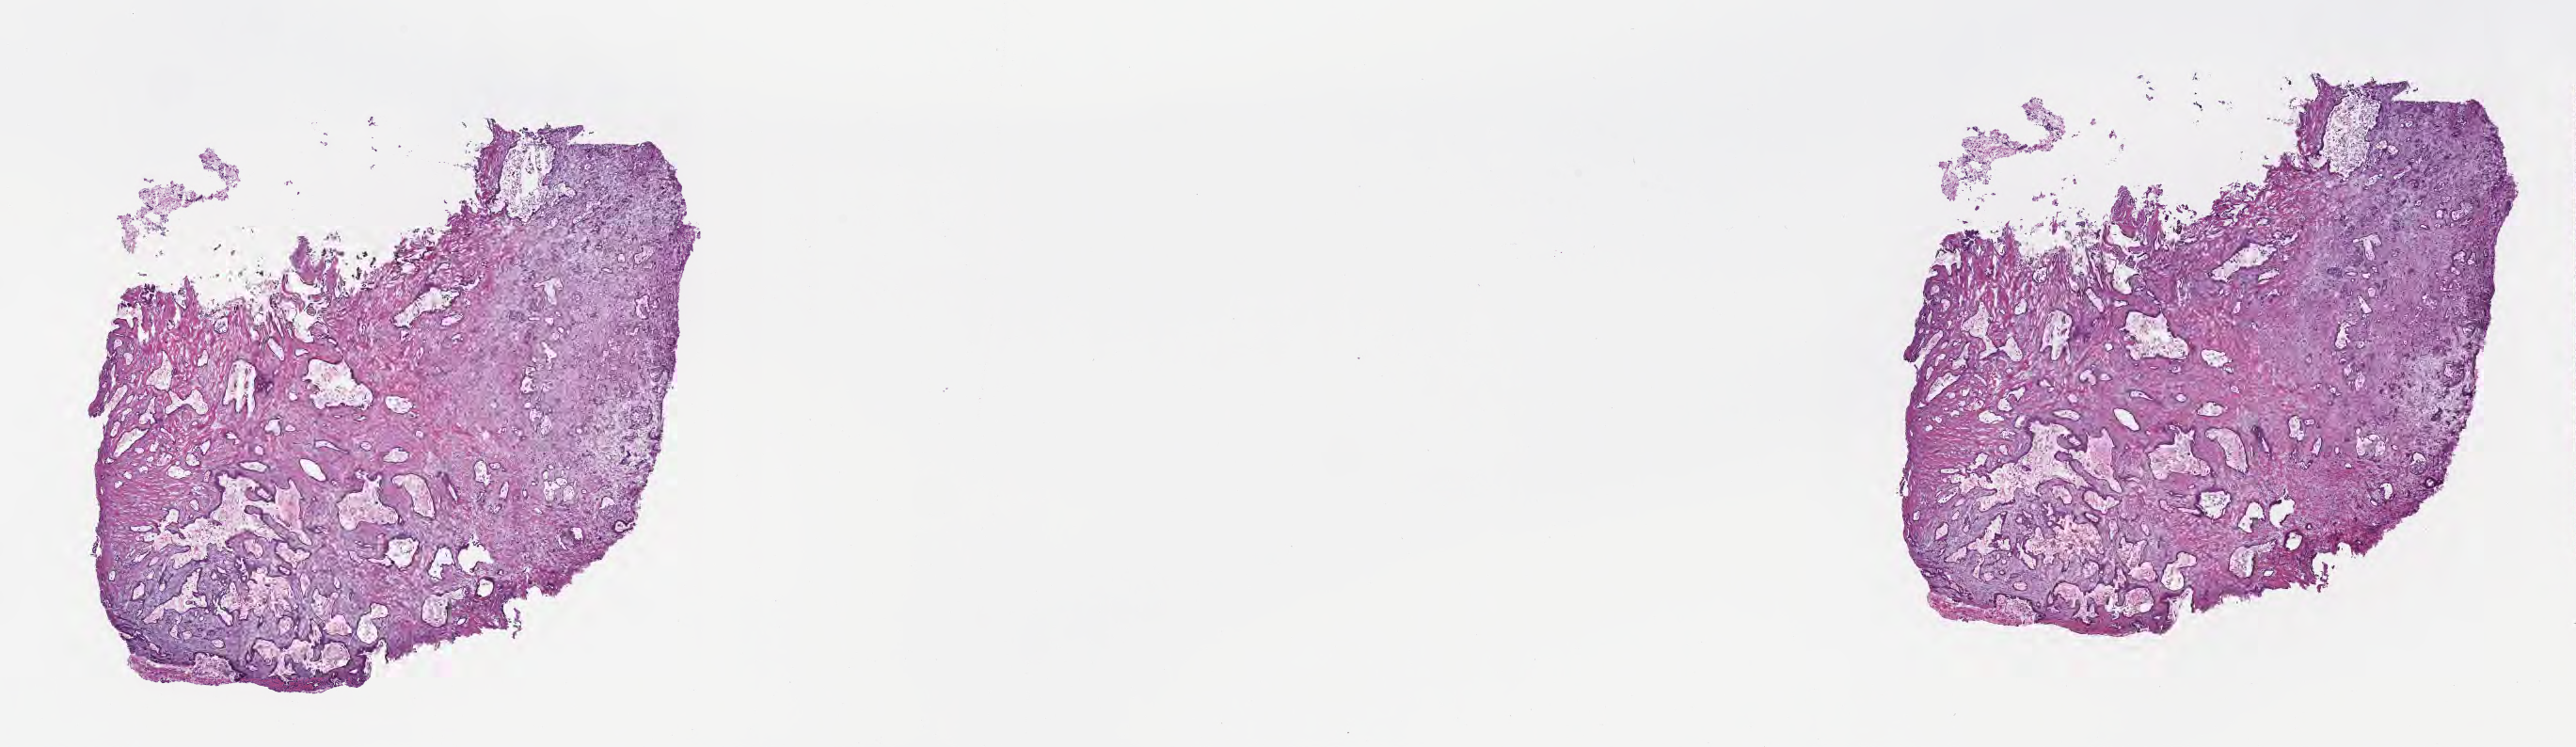
Digitized haematoxylin and eosin-stained section, low-resolution overview of the scanned area, about 22.1 x 6.4 mm; frozen section; specimen: primary tumor; anatomic site: tail of pancreas. Male patient; age at initial diagnosis 63 years. Slide review estimates, as recorded: tumor cells 100%, tumor nuclei 35%, stromal cells 0%, necrosis 0%, normal cells 0%. Inflammatory infiltration, as recorded: lymphocyte infiltration 0%, monocyte infiltration 0%, neutrophil infiltration 0%.
* diagnosis: Infiltrating duct carcinoma, NOS
* section: top of the tissue portion